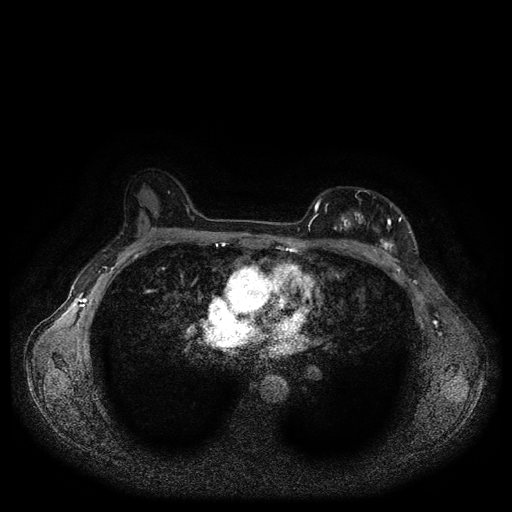
Breast MRI (dynamic contrast-enhanced, multi-phase), one axial slice. Position 67 of 116 along the scan axis. Dynamic contrast-enhanced series, time point 2 of 5 at this slice position (early post-contrast). 1.5 T. TE 2.6 ms, TR 5.3 ms. 2 mm slice thickness. 512 × 512 image matrix, field of view 350 × 350 mm. Patient: female, 51 years.
Outlined on this slice (semi-automatically segmented with operator editing):
- breast lesion (labelled 'tumour' in the annotation; benign lesions carry a separate 'benign' label): bounding box (x1, y1, x2, y2) in pixels: (330, 209, 399, 257)